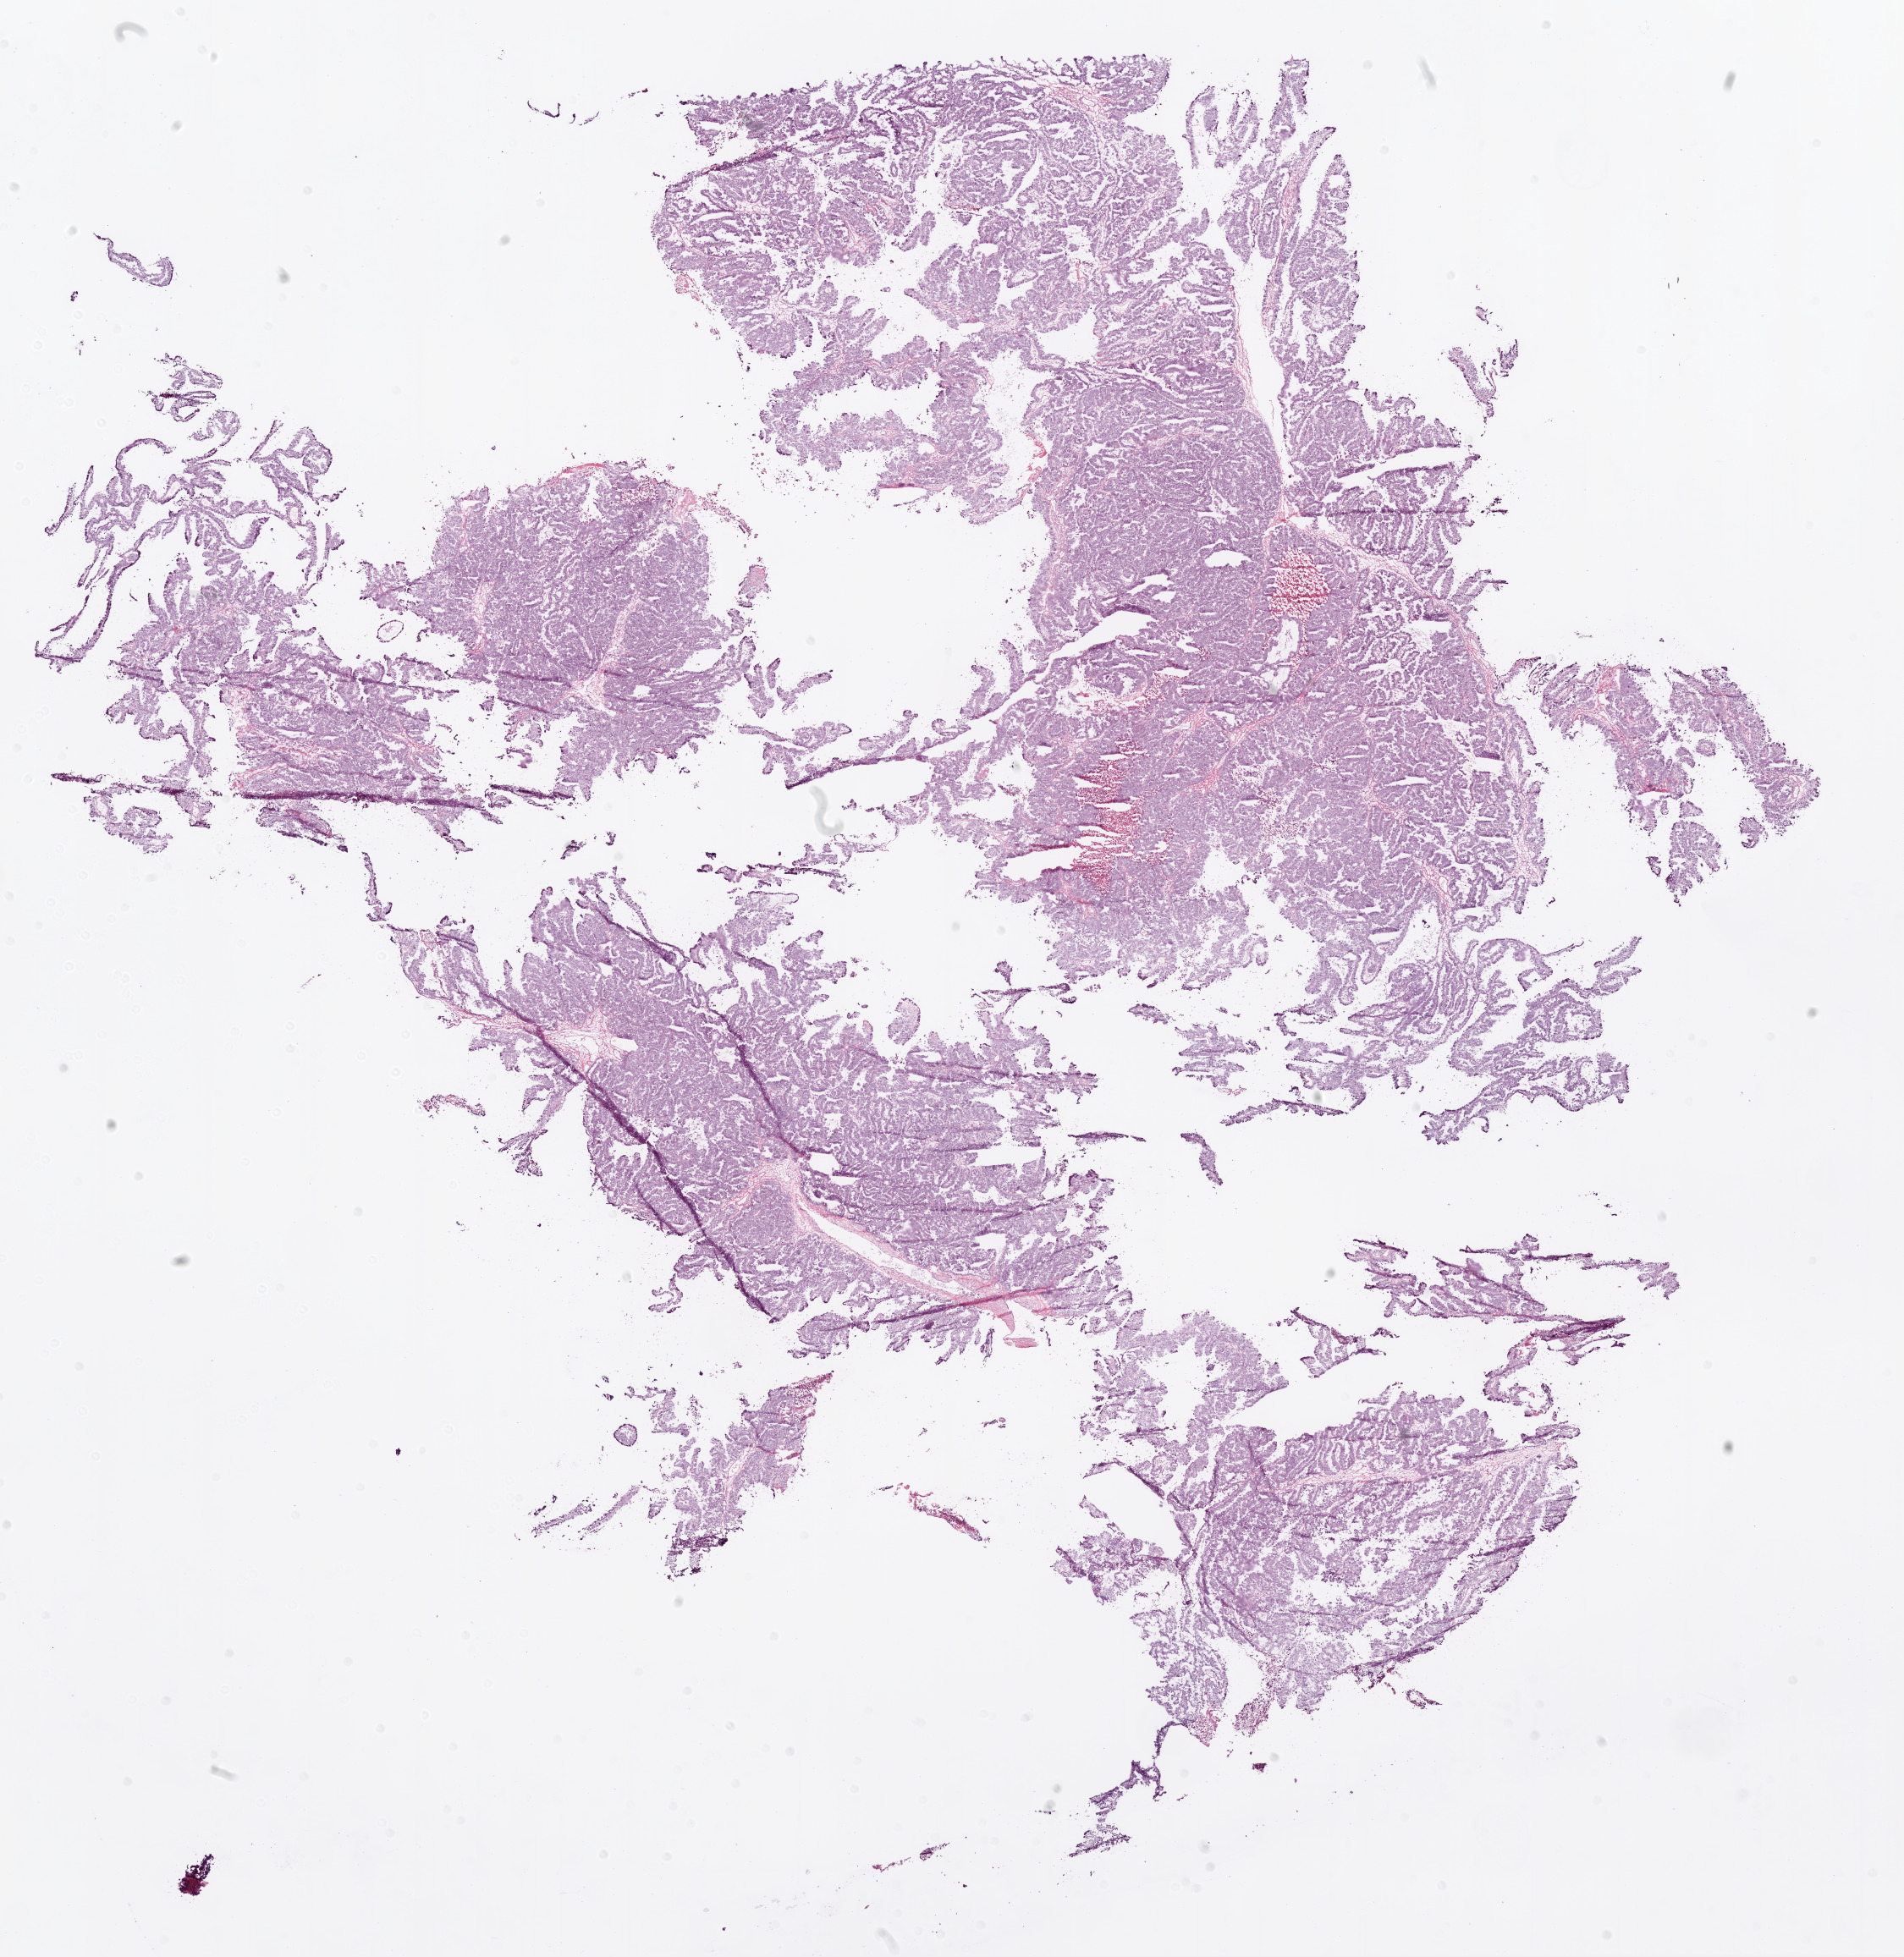
Whole-slide histology image, H&E-stained — low-resolution overview of the scanned area, about 18.1 x 18.6 mm, frozen section, sample: primary tumour, ovary. Female patient; age at initial diagnosis 79 years. Histologic grade: G3 (poorly differentiated). Pathologist review of this section (percent, as recorded): tumour cells 90%, tumour nuclei 99%, normal cells 0%, stromal cells 5%, necrosis 5%.
Laterality: bilateral. FIGO stage: IIIC. Pathologic diagnosis: Serous cystadenocarcinoma, NOS.